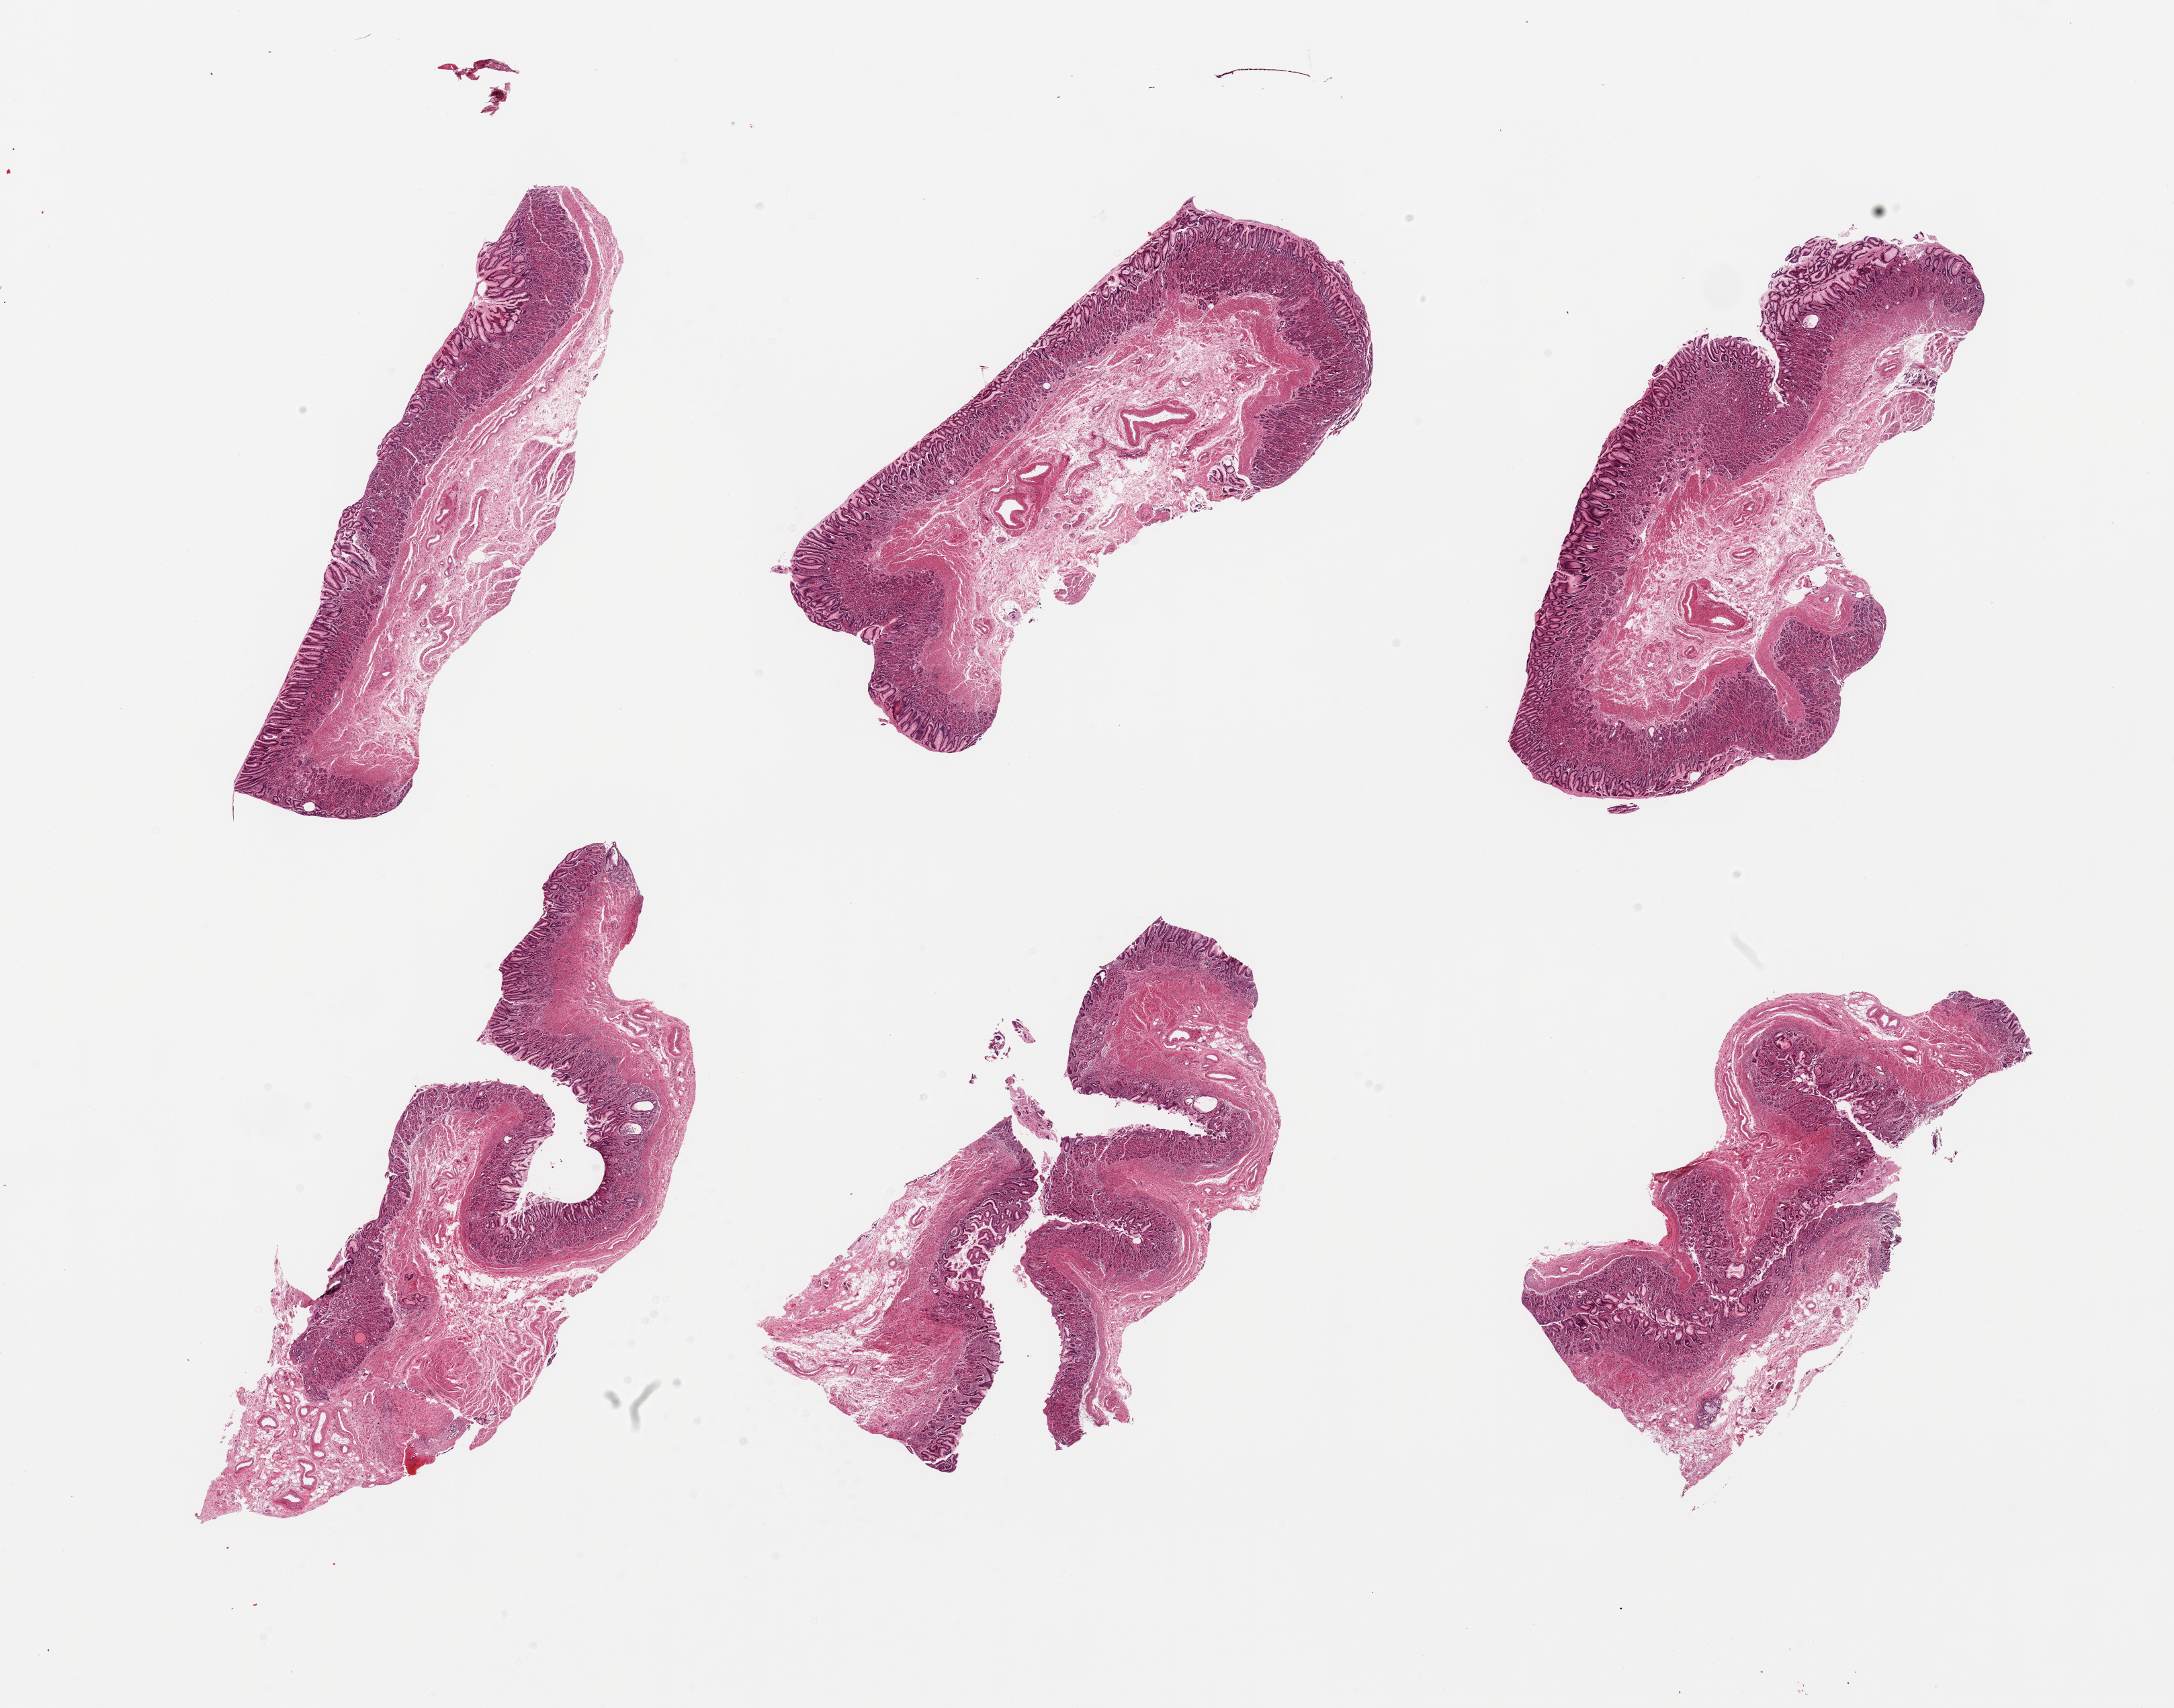
H&E whole-slide image, brightfield — shown as a low-resolution overview of the whole scanned area (about 25.6 x 20.1 mm, slide scanned at 20x). PAXgene-fixed paraffin-embedded (PFPE) section. Sampled site (target tissue): gastroesophageal junction. Donor tissue sample. Male donor.
• review note (as recorded): 6 pieces; stomach, not GE junction, predominantly mucosa with scant attached muscularis, chronic active gastritis